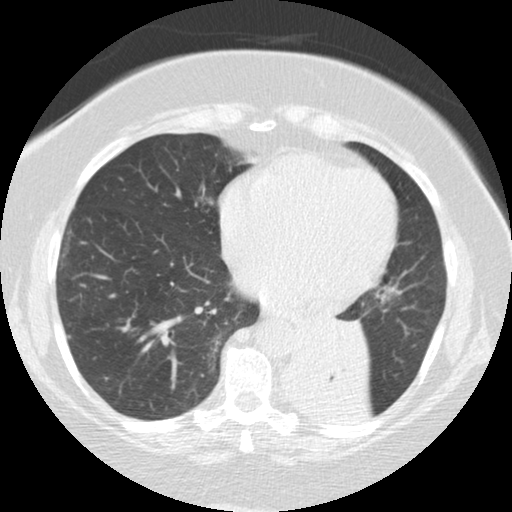
Low-dose screening chest CT, axial slice. Baseline screening round. Lung window (W 1500 / L -600 HU). 2.5 mm slice thickness. Standard (soft-tissue) reconstruction kernel (STANDARD). Slice 81 of 136 in the series. 512 × 512 image matrix, field of view 309 × 309 mm. Female participant, aged 71 years at enrolment.
Expert-annotated lung lesion, bounding box (x1, y1, x2, y2) in pixels: (278, 301, 371, 384). Reader record for this screening exam (exam-level; its link to the box is not recorded): non-calcified nodule or mass ≥4 mm, right middle lobe, 5 × 5 mm, smooth margins, soft tissue attenuation. Note: the box lies in the patient's left hemithorax on this image, whereas the reader's record names the right lung; they may be different findings. Official screen result: positive, change unspecified: nodule(s) >= 4 mm or enlarging nodule(s), mass(es), or other non-specific abnormalities suspicious for lung cancer. Participant outcome: lung cancer diagnosed 46 days after this screen — large cell carcinoma, NOS, left lower lobe, mediastinum, other location, poorly differentiated (G3), stage IV (AJCC 6th edition), 50 mm at pathology.